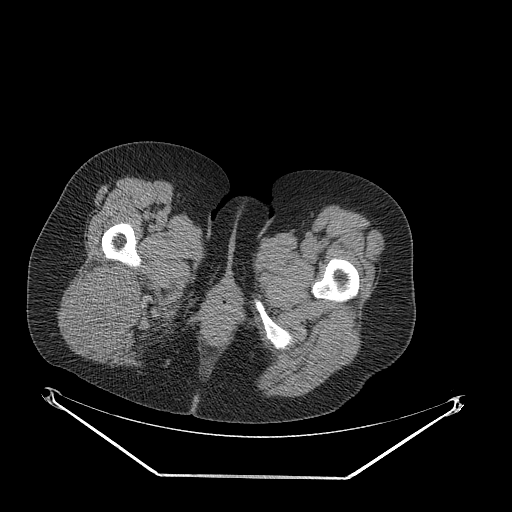
CT of an extremity soft-tissue mass (from a PET/CT study), one axial slice. Slice 52 of 257 in the series (ordered by position). 140 kVp. Soft-tissue window (W 400 / L 40 HU). 512 × 512 image matrix. Female patient. From the clinical record (not read from this slice): histological type: synovial sarcoma; grade: intermediate; site of the primary tumour: right buttock.
Structures marked on this image (expert contour drawn on MRI and transferred to this co-registered scan by the dataset authors):
- gross tumour volume including surrounding oedema: bounding box [x1, y1, x2, y2] px = [69, 260, 145, 352]
- gross tumour volume (mass): [69, 260, 145, 352]